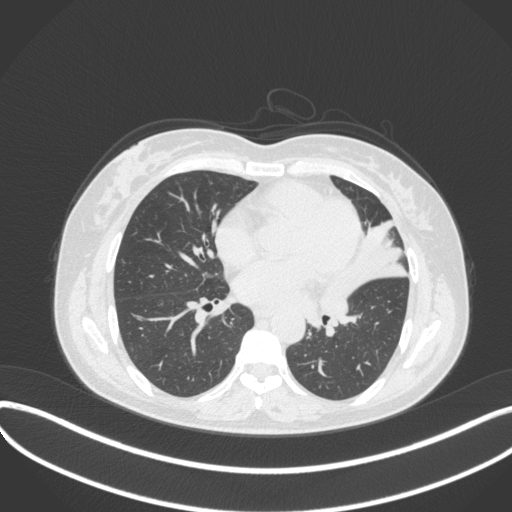
Chest CT, one axial slice; slice 164 of 373 in the series (ordered by position); lung window (W 1500 / L -600 HU); 1 mm slice thickness; 512 × 512 image matrix. Female patient, age 54 years. From the clinical record (not read from this slice): clinical TNM (as recorded): T2a N1 M0; histopathological grade: G3.
Structures marked on this image (bounding box drawn by a radiologist):
- lung tumour (recorded histology: small cell carcinoma): bounding box [x1, y1, x2, y2] px = [315, 273, 356, 320]